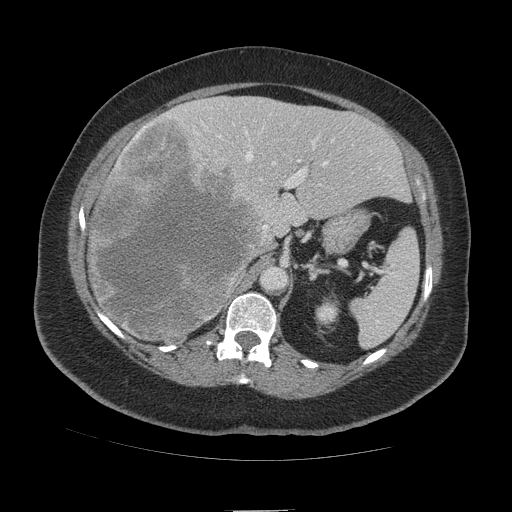
Contrast-enhanced abdominal CT (liver protocol), one axial slice; position 66 of 109 along the scan axis; reconstruction kernel STANDARD; soft-tissue window (W 400 / L 40 HU); 2.5 mm slice thickness; 512 × 512 image matrix, field of view 420 × 420 mm. From the clinical record (not read from this slice): diagnosis: hepatocellular carcinoma (patient treated with transarterial chemoembolisation; whether this scan precedes or follows treatment is not stated here); TNM stage (as recorded): Stage-IVB; Child-Pugh class: A; tumour differentiation: poorly differentiated.
Structures marked on this image (semi-automatically segmented with operator editing):
- liver parenchyma outside the tumour (the mass and vessels are separate outlines, so this box may not span the whole liver): bounding box <88,96,408,336> (left, top, right, bottom; pixels)
- mass: <88,118,263,346>
- liver vessels: <135,114,334,231>